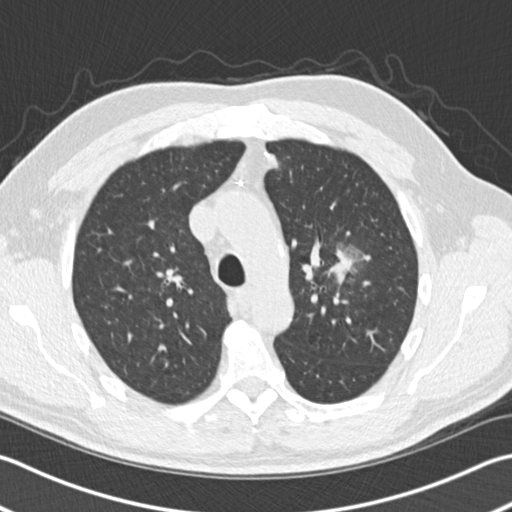
Chest CT (low-dose screening protocol), one axial image; third annual screen; lung window (W 1500 / L -600 HU); slice 43 of 153 in the series; 512 × 512 image matrix, field of view 346 × 346 mm. Male participant, aged 65 years at enrolment. Former smoker at enrolment.
Expert-annotated lung lesion, bounding box [x1, y1, x2, y2] px = [306, 240, 370, 305]. The screening reader recorded 4 non-calcified nodules or masses ≥4 mm on this exam; which of them this box marks is not recorded. Lung cancer was diagnosed 196 days after this screen: acinar cell carcinoma, left upper lobe, stage IA (AJCC 6th edition), 25 mm at pathology.